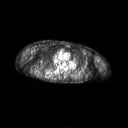
FDG PET of an extremity soft-tissue mass (from a PET/CT study), one axial slice; slice 176 of 267 in the series (ordered by position); 3.27 mm slice thickness; 128 × 128 image matrix. Male patient, age 61 years. Case-level facts recorded for this patient, not image findings: histological type: pleiomorphic spindle cell undifferentiated; grade: high; site of the primary tumour: right parascapusular.
Annotated regions visible in this slice (expert contour drawn on MRI and transferred to this co-registered scan by the dataset authors):
- gross tumour volume including surrounding oedema: box from (x=46, y=73) to (x=59, y=78) px